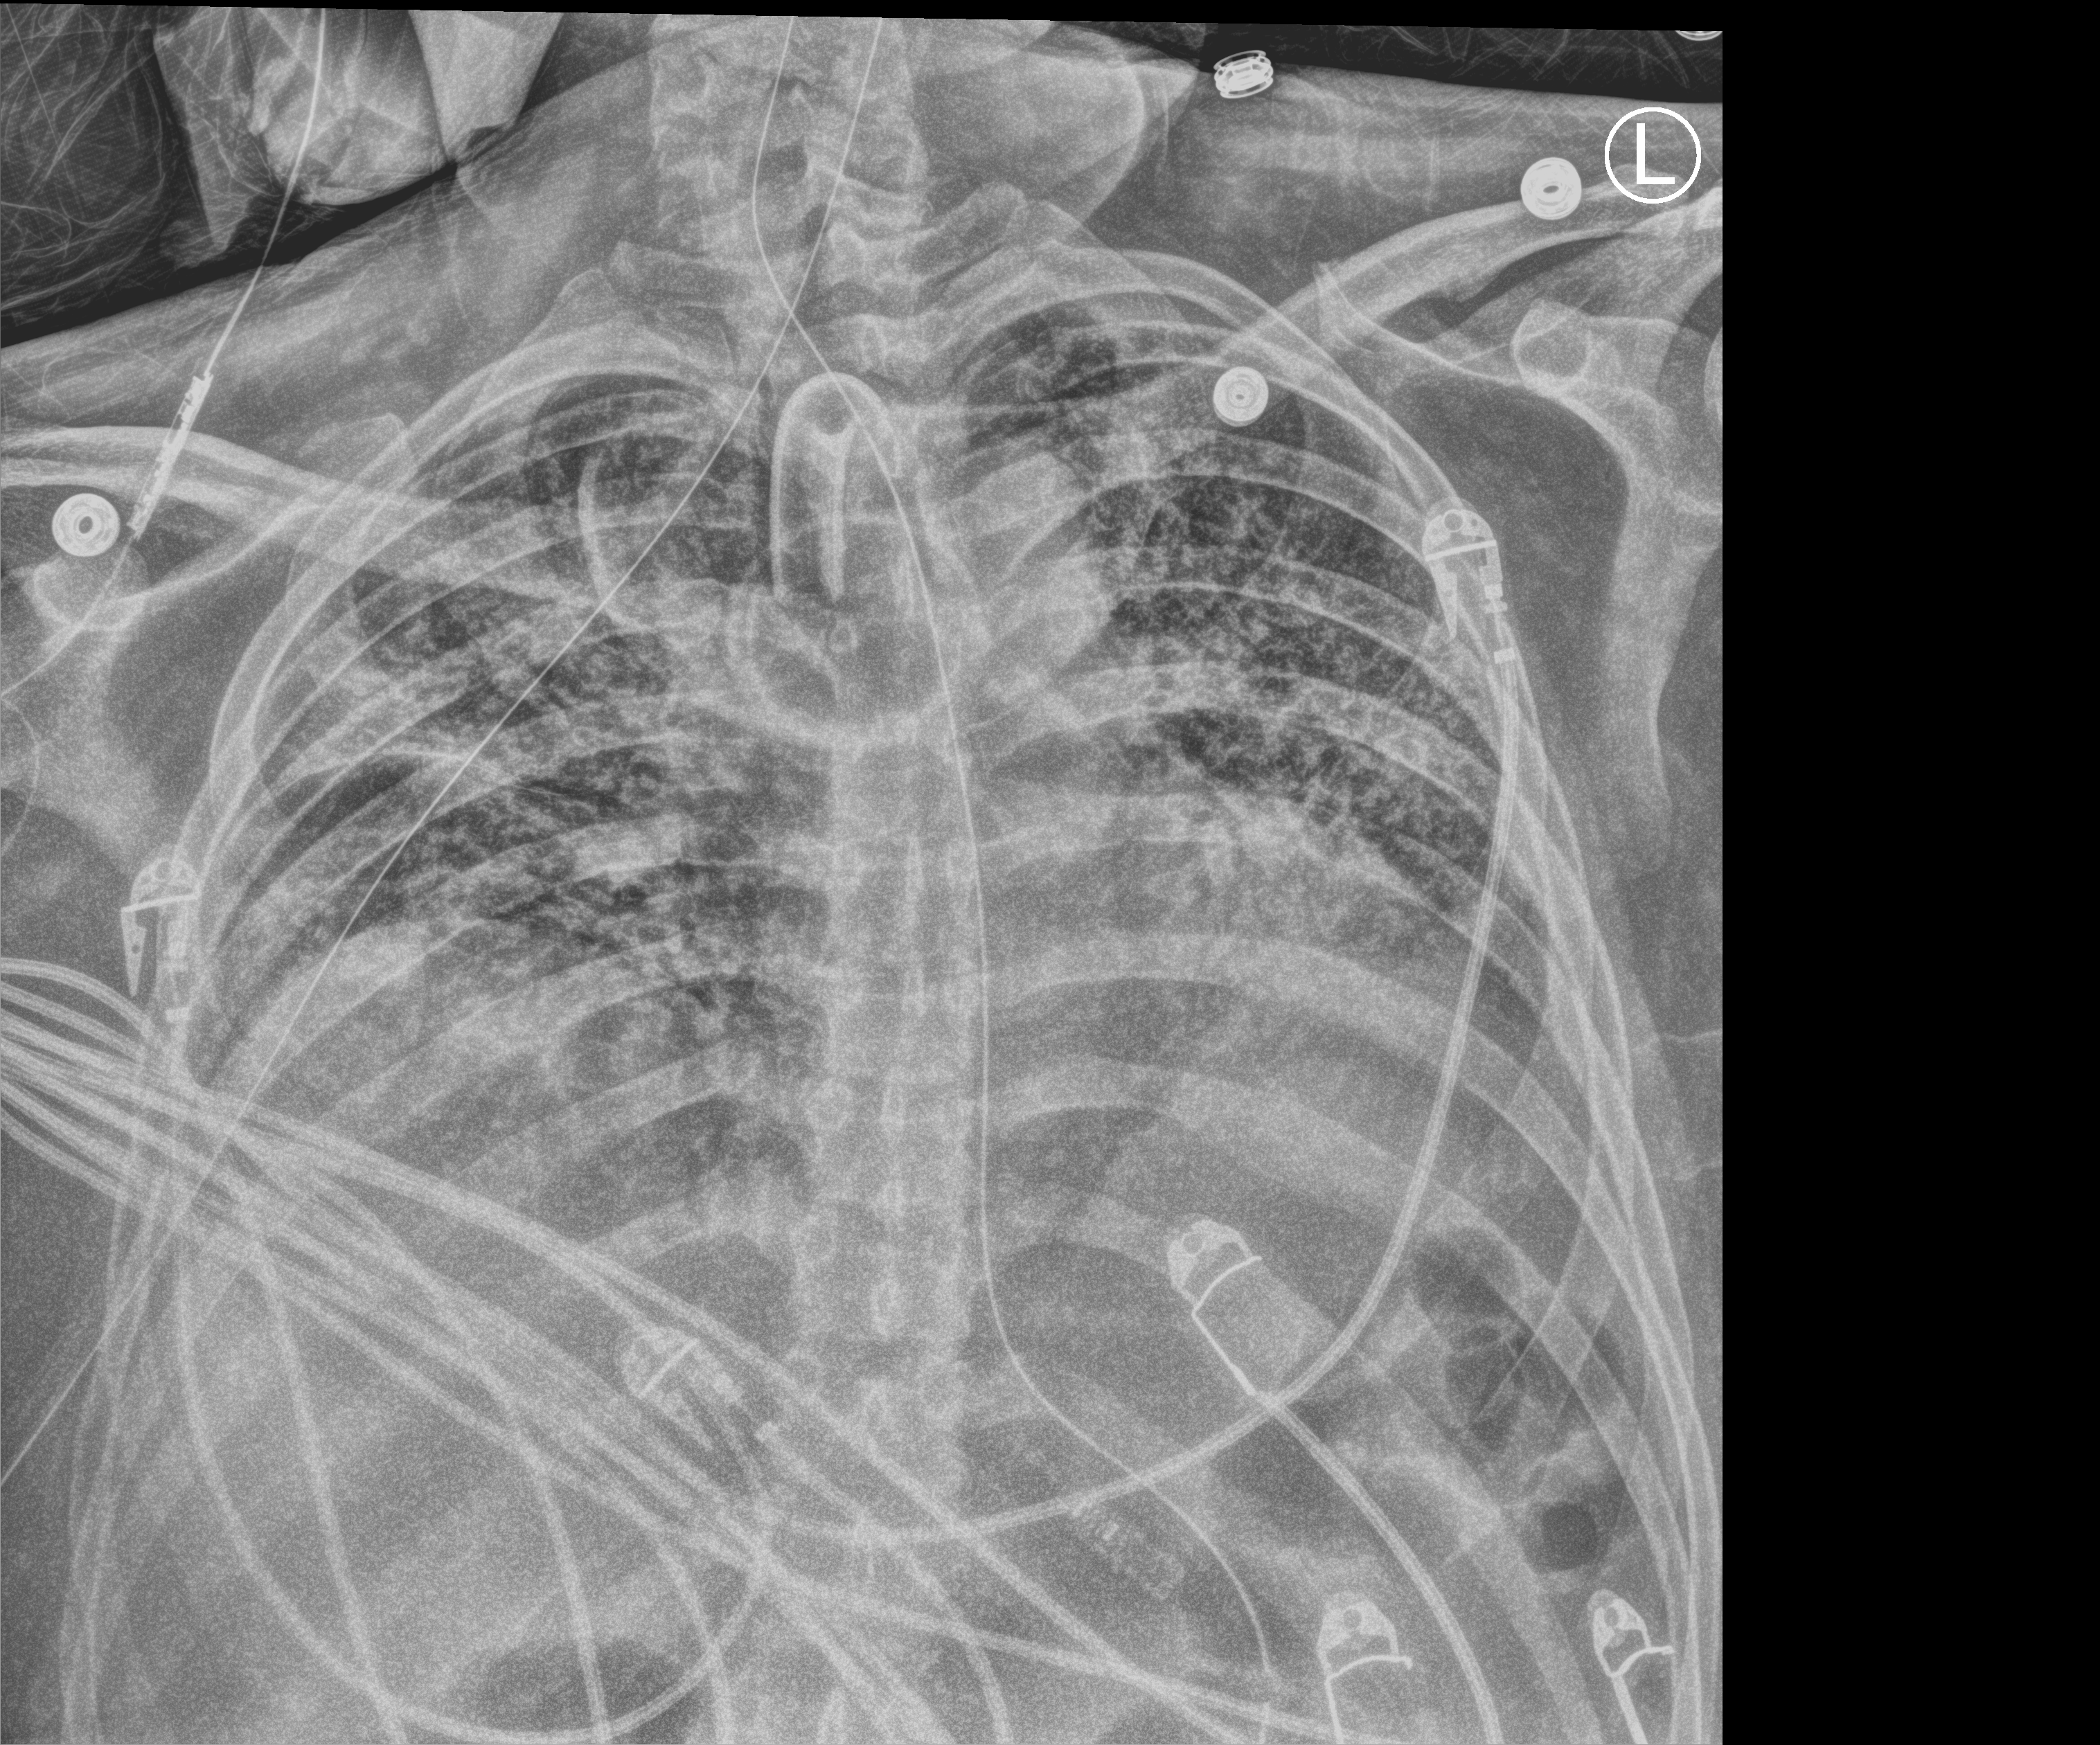
Bedside chest radiograph (computed radiography); anteroposterior (AP) projection. Male patient hospitalised with COVID-19, age 18–59 years.
Admission-level facts for this patient (not findings on this image; timing relative to this image not recorded): mechanically ventilated during this hospital stay: yes; admitted to intensive care during this hospital stay: yes.